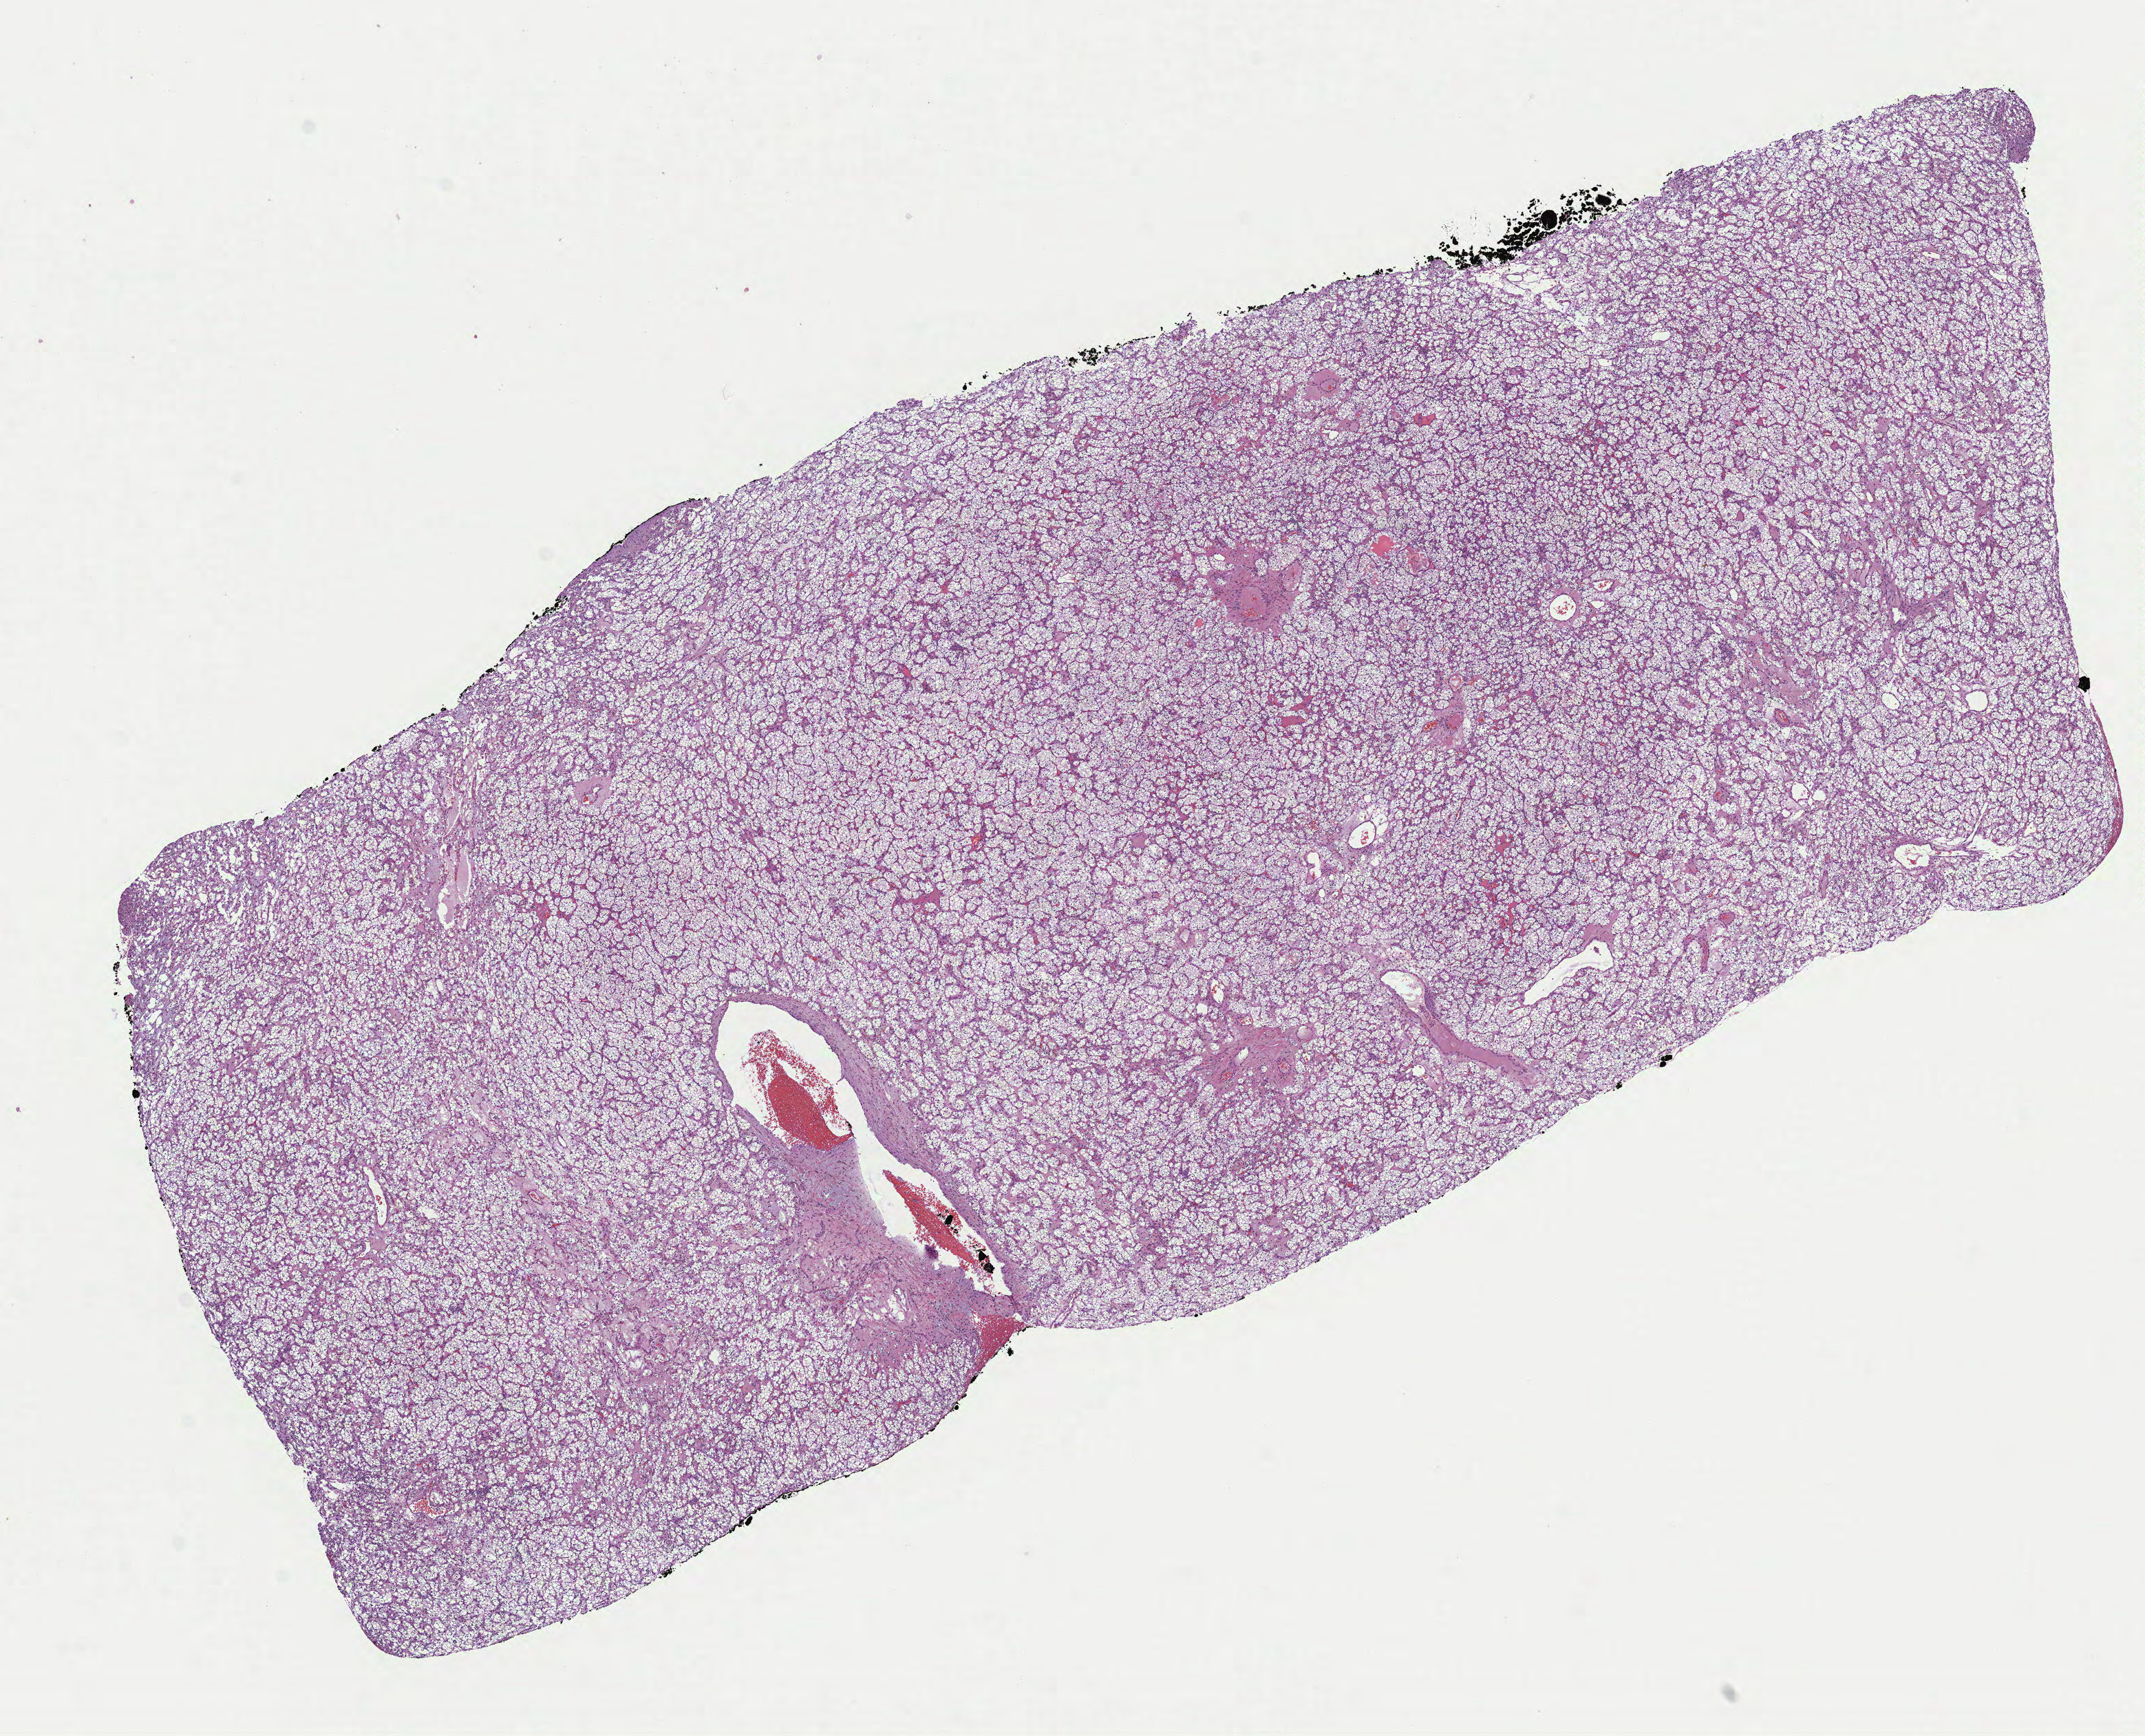
Whole-slide histology image, H&E-stained, whole scanned area (about 12.6 x 10.2 mm, acquisition: 40x scan) shown as a low-resolution overview, FFPE section, sample: primary tumour, kidney. Patient: female, age at initial diagnosis 49 years. Histologic grade: G2 (moderately differentiated).
Pathologic diagnosis: Renal cell carcinoma, NOS. Laterality: left. TNM: T1b NX MX. AJCC pathologic stage: I (7th edition).